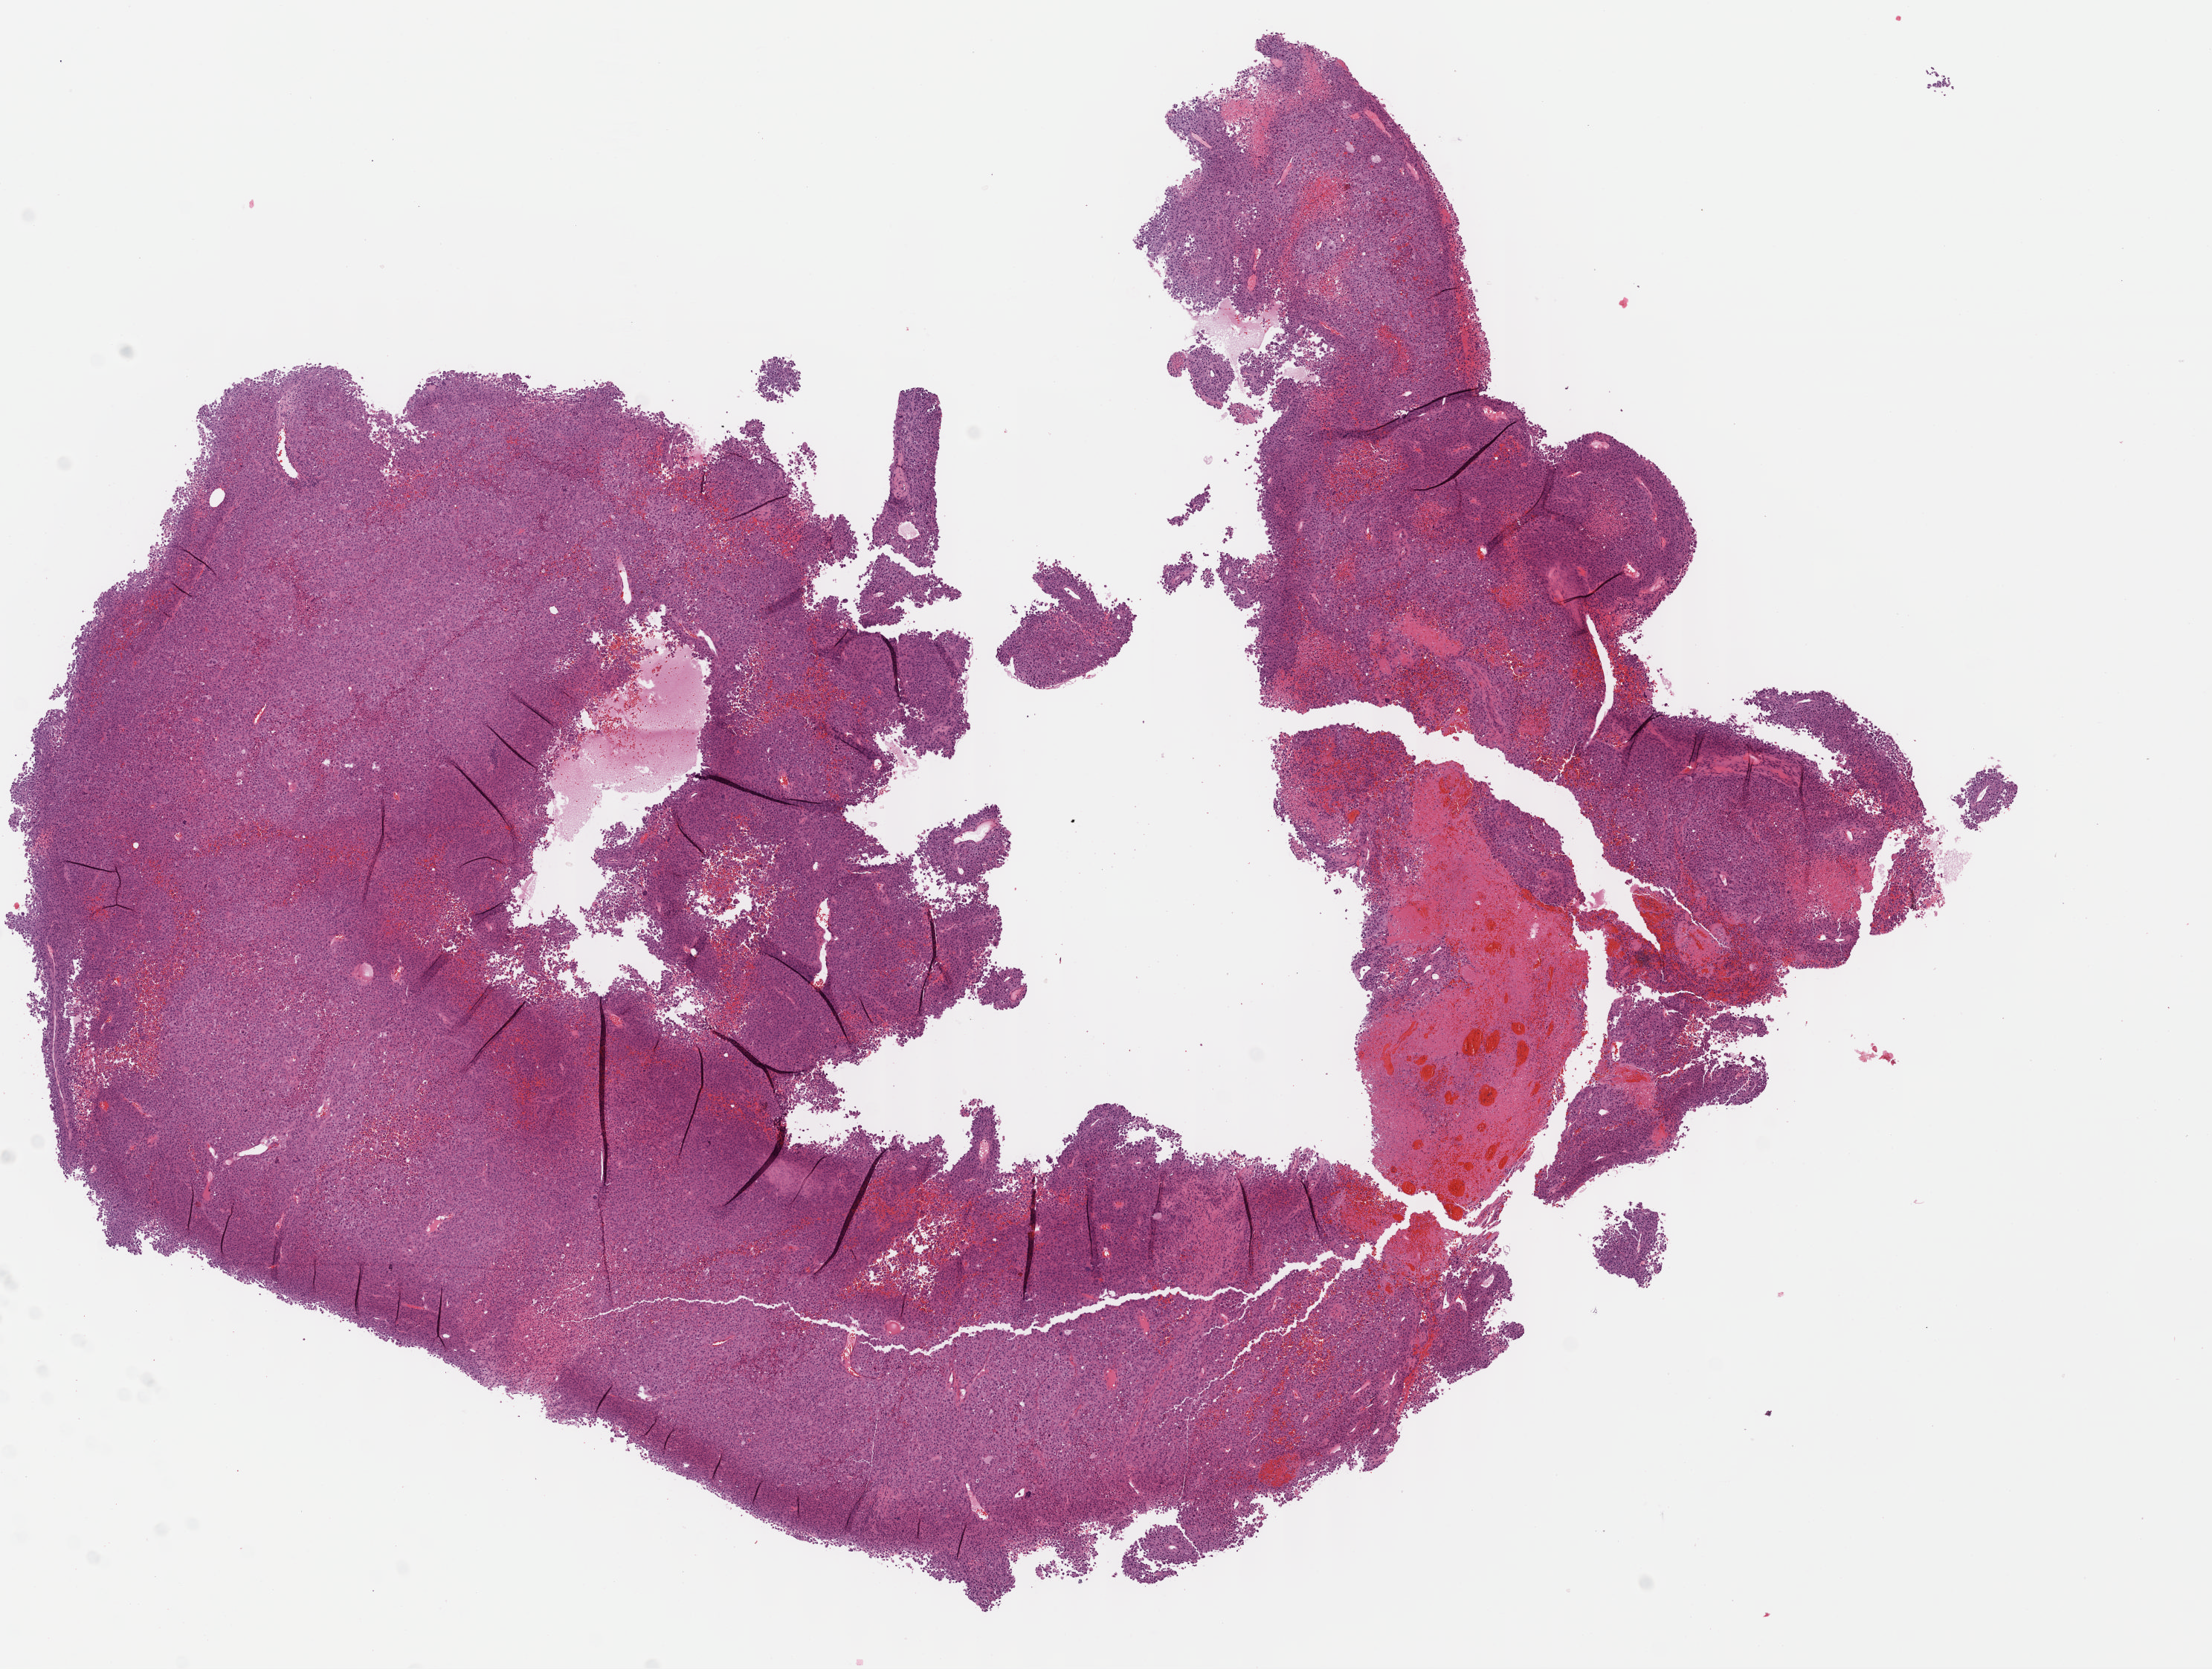
H&E whole-slide image — a low-resolution overview of the entire scanned area, about 11.7 x 8.8 mm (acquisition: 40x scan); FFPE section; metastatic tumour sample, sampled site: lymph nodes of axilla or arm. Female, age 62 years at initial diagnosis.
• this section: metastatic tumour tissue
• patient diagnosis: Malignant melanoma, NOS